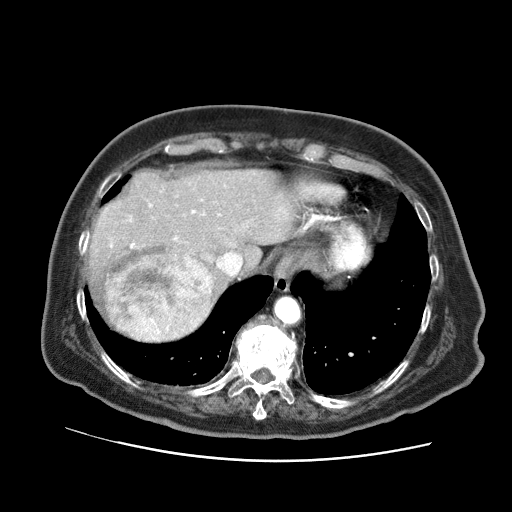
Contrast-enhanced abdominal CT (liver protocol), one axial slice. Position 55 of 73 along the scan axis. Reconstruction kernel STANDARD. 120 kVp. Soft-tissue window (W 400 / L 40 HU). 2.5 mm slice thickness. 512 × 512 image matrix, field of view 380 × 380 mm. Case-level facts recorded for this patient, not image findings: diagnosis: hepatocellular carcinoma (patient treated with transarterial chemoembolisation; whether this scan precedes or follows treatment is not stated here); TNM stage (as recorded): Stage-I; Child-Pugh class: A; tumour differentiation: well differentiated.
Structures marked on this image (semi-automatically segmented with operator editing):
- liver parenchyma outside the tumour (the mass and vessels are separate outlines, so this box may not span the whole liver): box from (x=84, y=168) to (x=300, y=342) px
- mass: (x=103, y=244)–(x=216, y=341)
- liver vessels: (x=110, y=204)–(x=221, y=248)